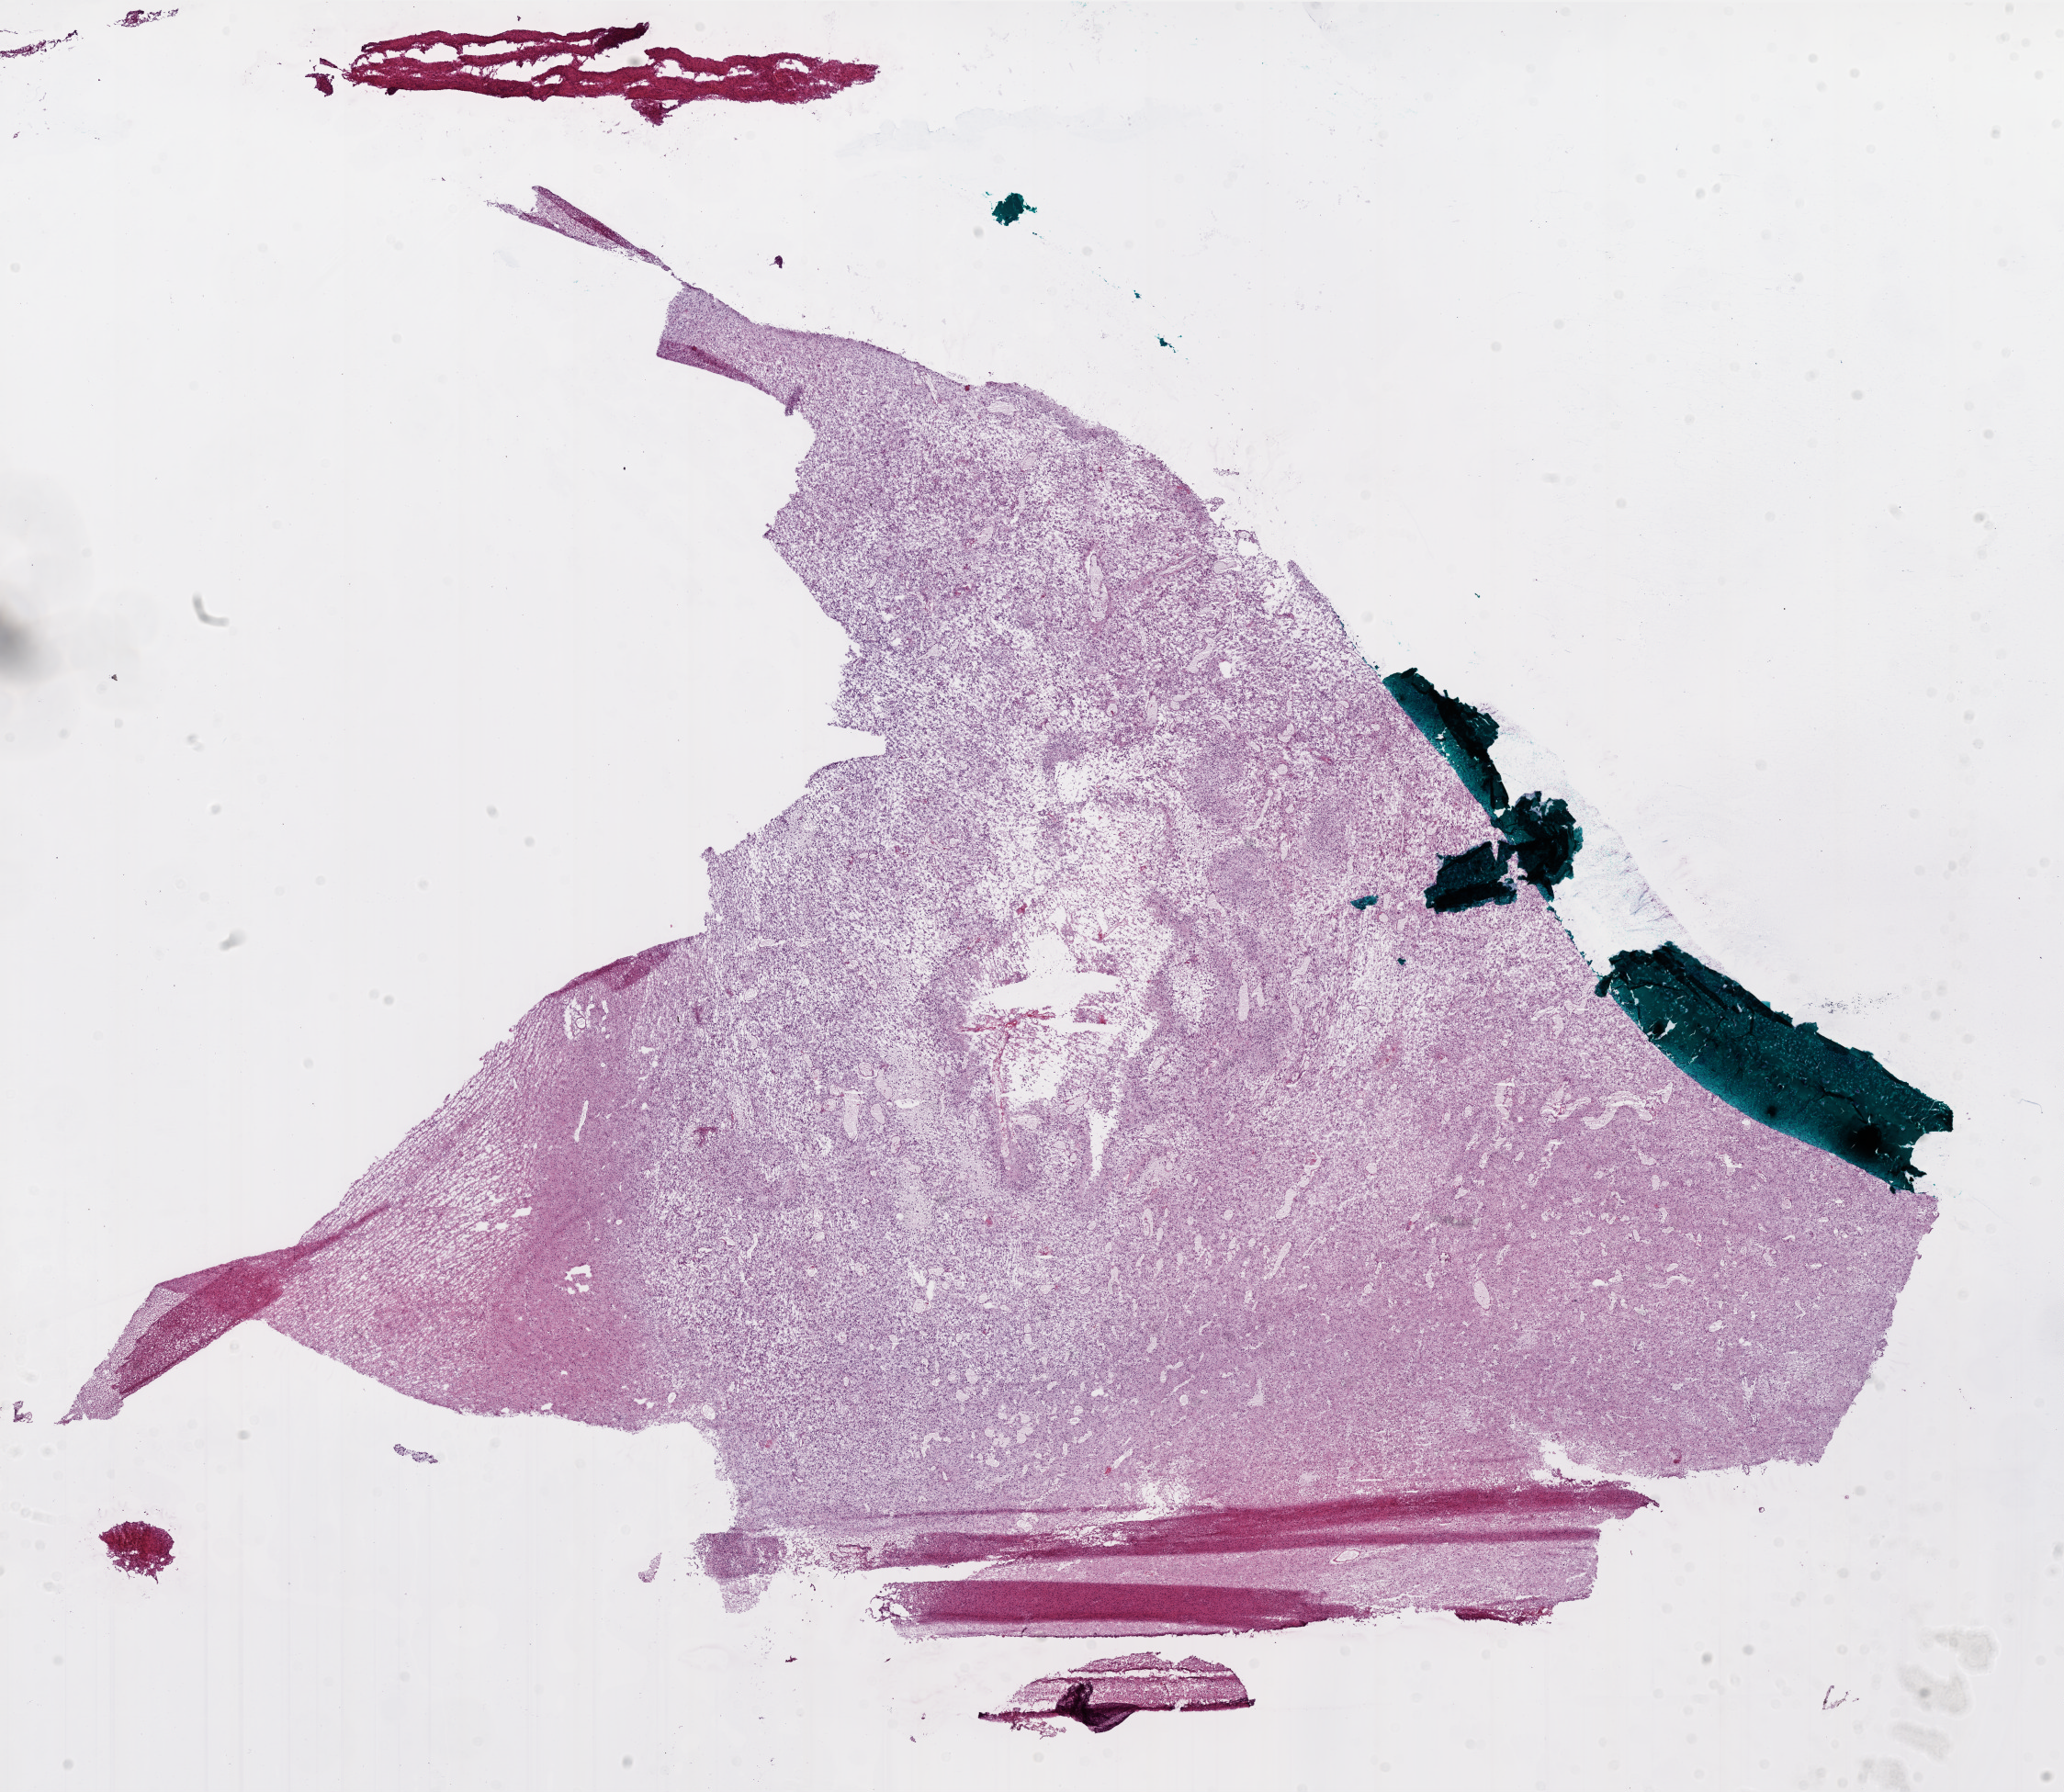
Whole-slide histology image, H&E, shown as a low-resolution overview of the whole scanned area (about 18.0 x 15.6 mm, slide scanned at 20x), frozen section, primary tumour sample from the brain. Female, age 62 years at initial diagnosis. Pathologist review of this section (percent, as recorded): tumour cells 75%, tumour nuclei 95%, normal cells 0%, stromal cells 20%, necrosis 5%. Infiltration values recorded for this section: lymphocyte infiltration 0%.
* pathologic diagnosis: Glioblastoma